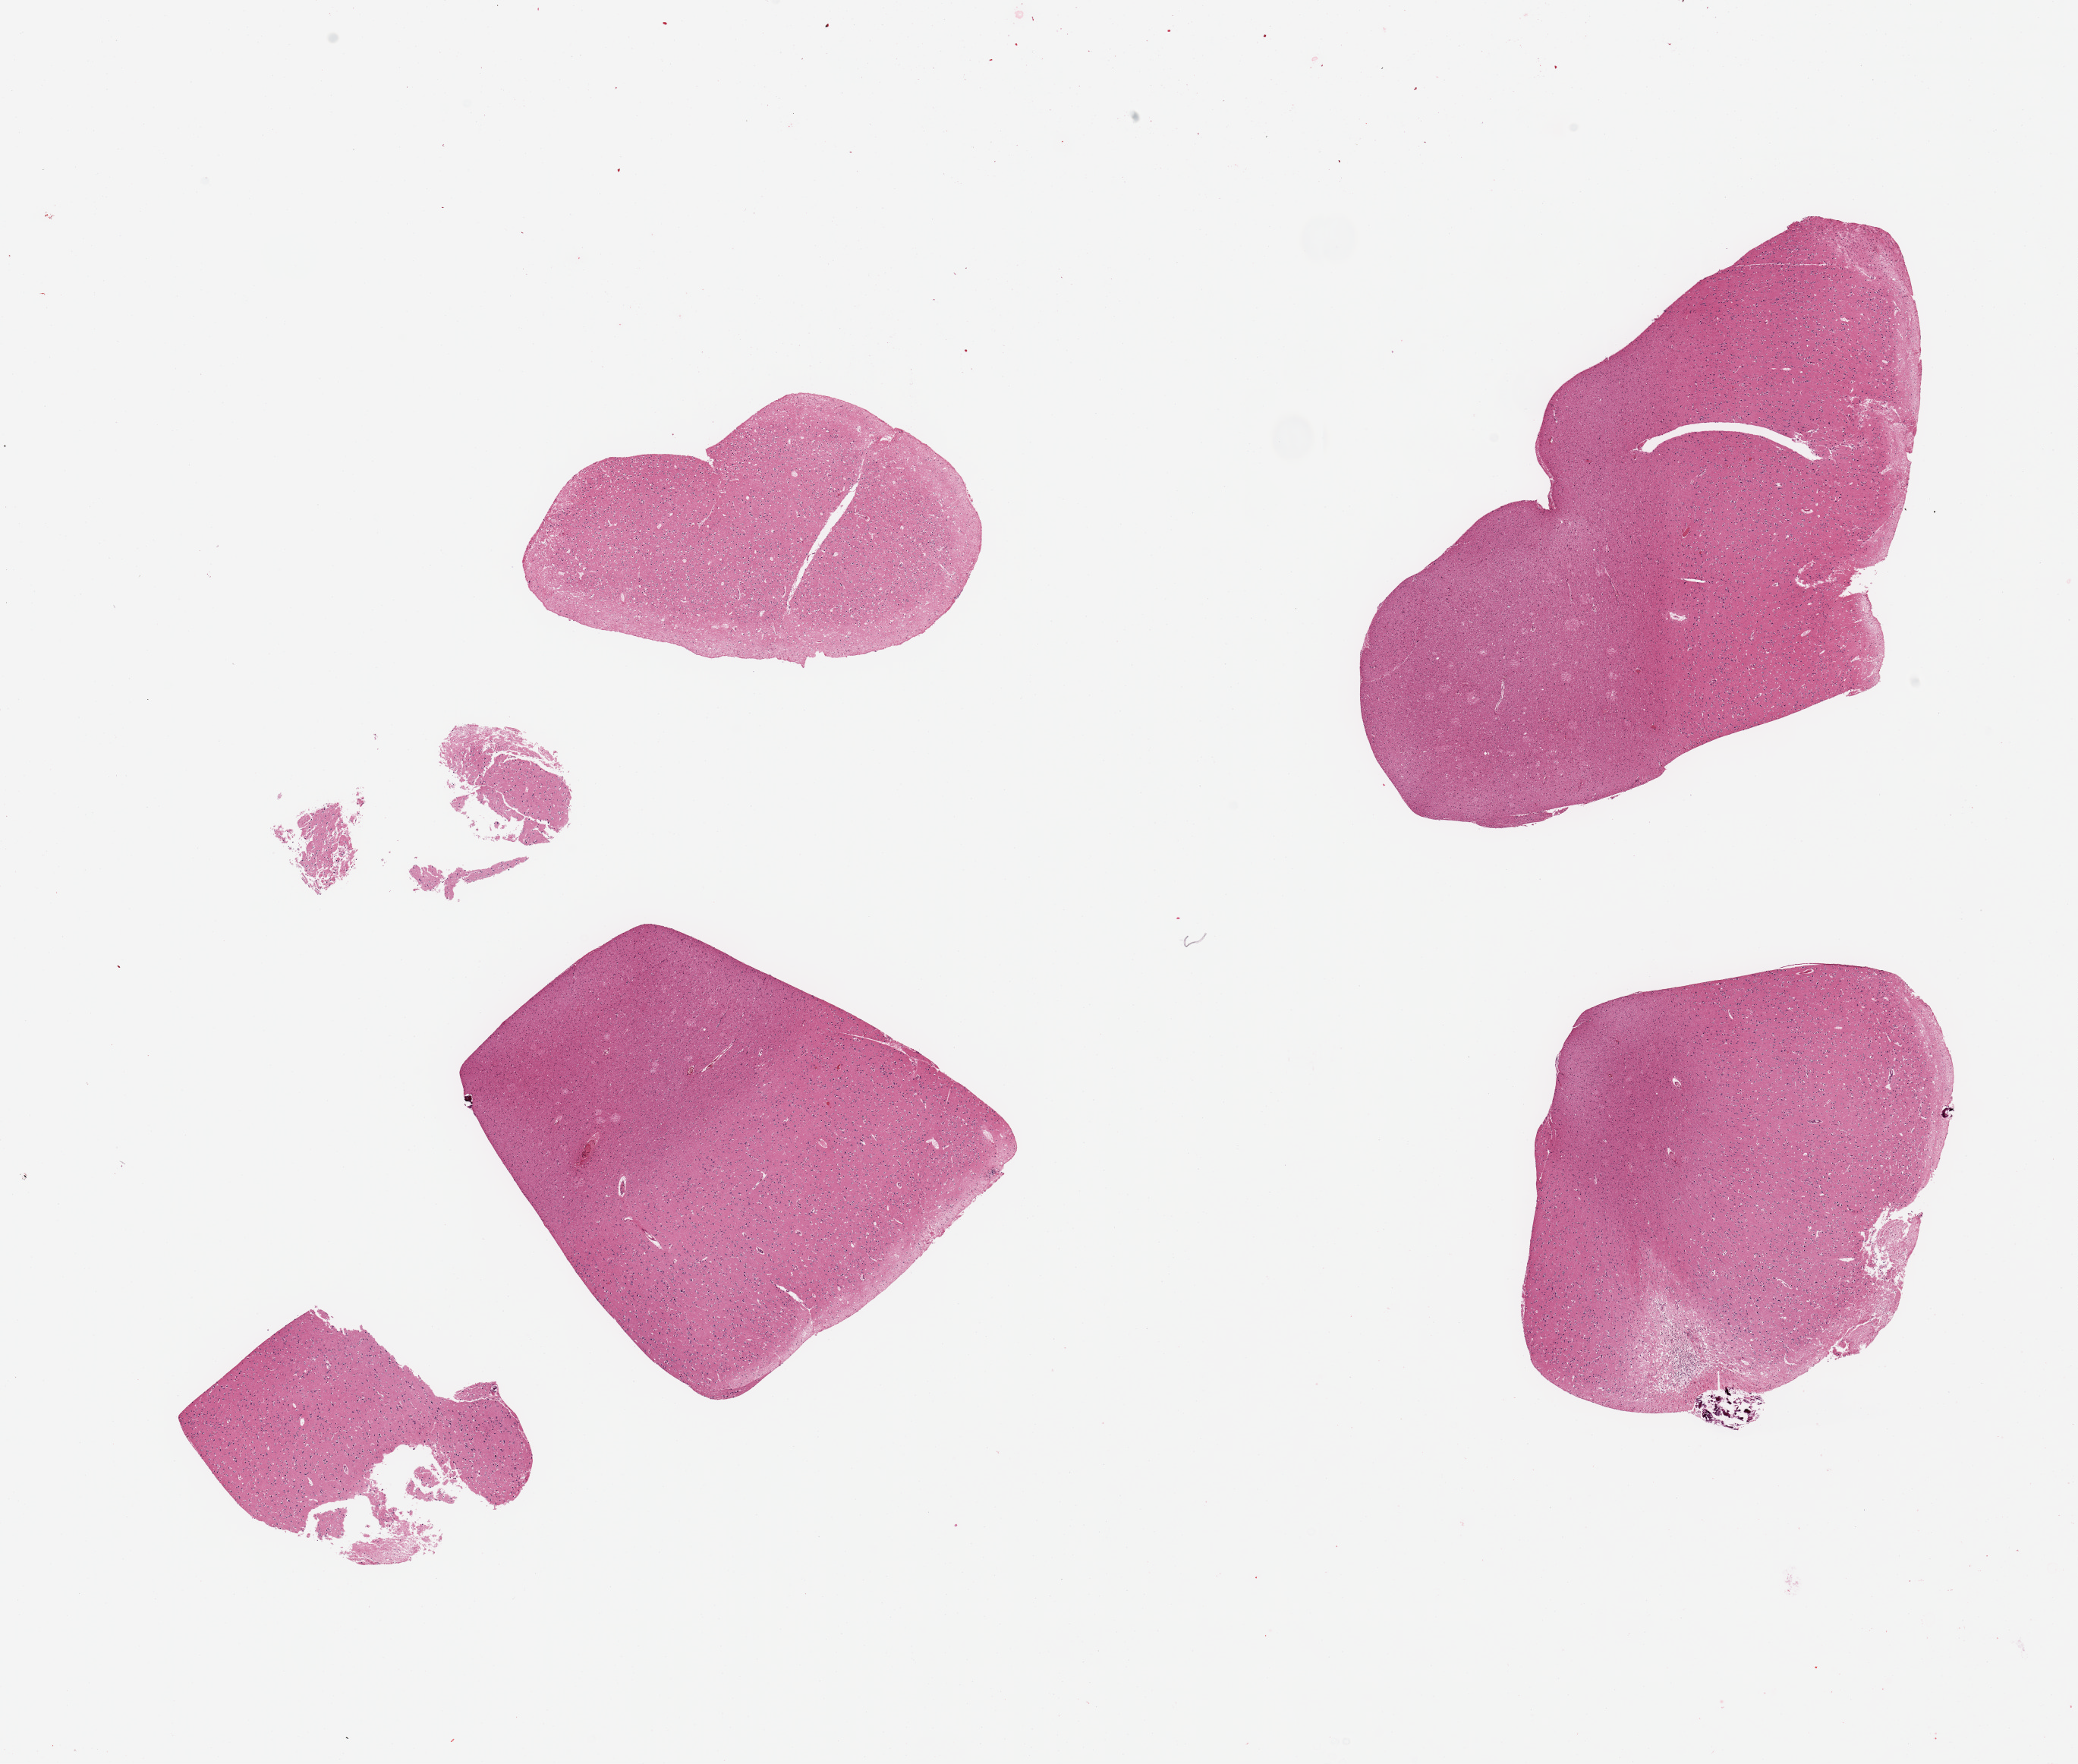
H&E whole-slide image — shown as a low-resolution overview of the whole scanned area (about 21.7 x 18.4 mm, slide scanned at 20x), PAXgene-fixed, paraffin-embedded tissue, sampled site (target tissue): cerebral cortex, donor tissue sample.
Pathologist's review note for this sample: 4 pieces; small focus of pigmented macrophages with surrounding edema, consistent with old infarct.